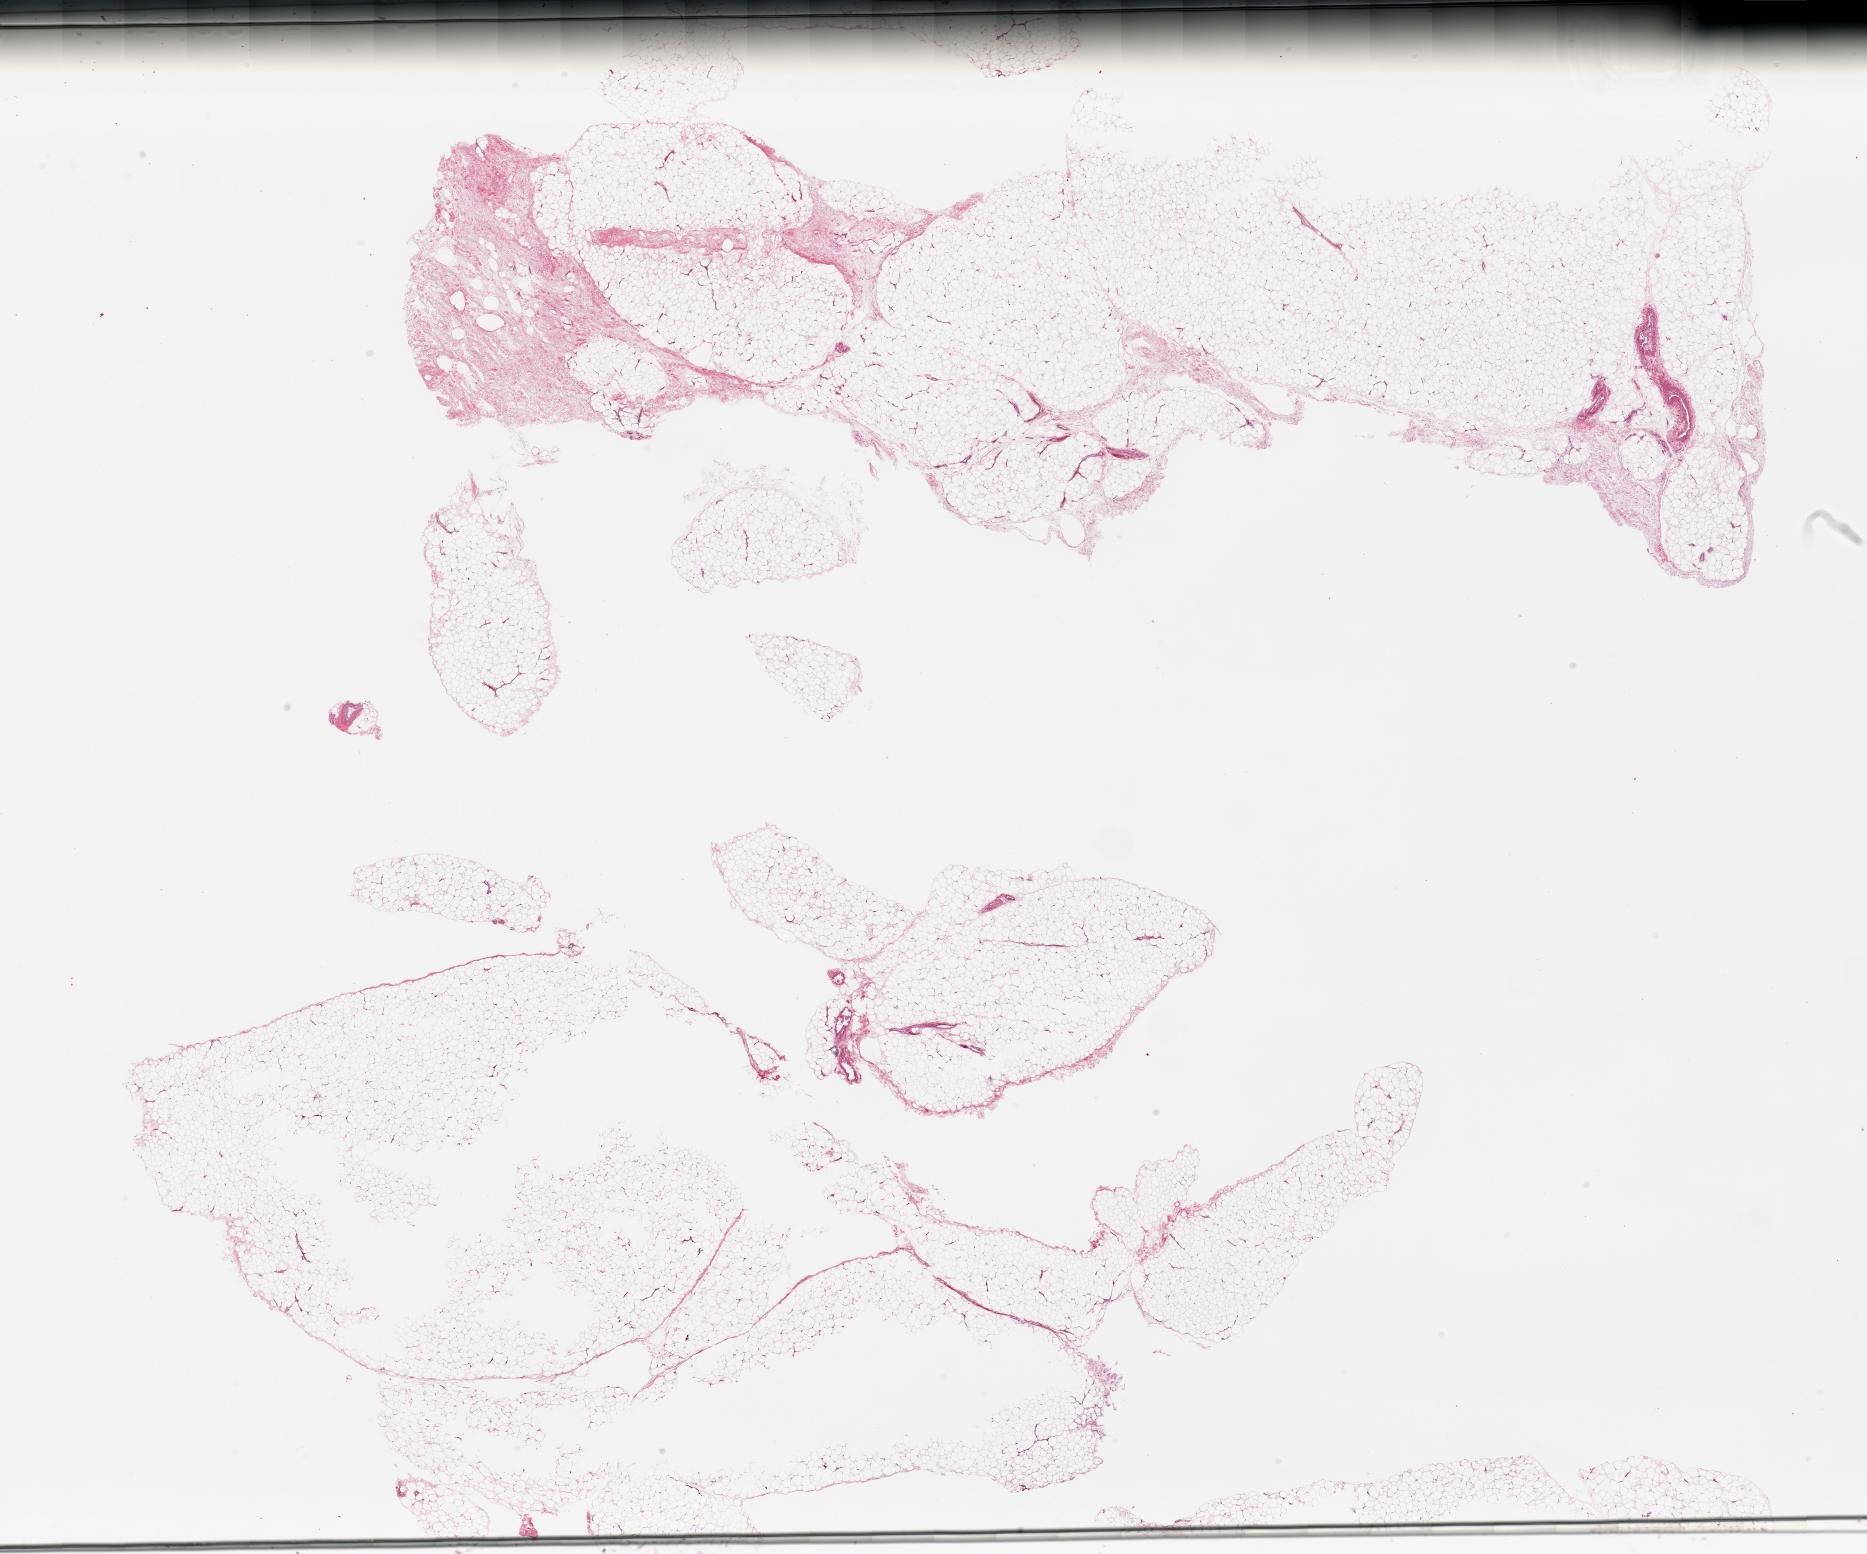
Whole-slide image, H&E stain, a low-resolution overview of the entire scanned area, about 29.5 x 24.6 mm, PAXgene-fixed, paraffin-embedded tissue, sampled site (target tissue): adipose tissue, tissue donor sample. Donor: male.
Reviewer comment on this tissue sample: 2 pieces (fragmented); oversized with central defects in one piece.